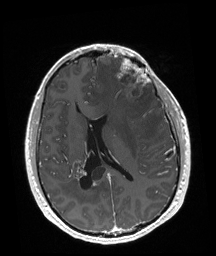
Brain MRI from a brain-tumour surgery series, one axial slice. Slice 81 of 192 in the series (ordered by position). T1-weighted post-contrast. 1 mm slice thickness. 216 × 256 image matrix, field of view 219 × 260 mm. From the clinical record (not read from this slice): tumour location: Left Frontal.
Outlined on this slice (outlined manually by an expert reader):
- tumour: bounding box [x1, y1, x2, y2] px = [116, 58, 151, 103]